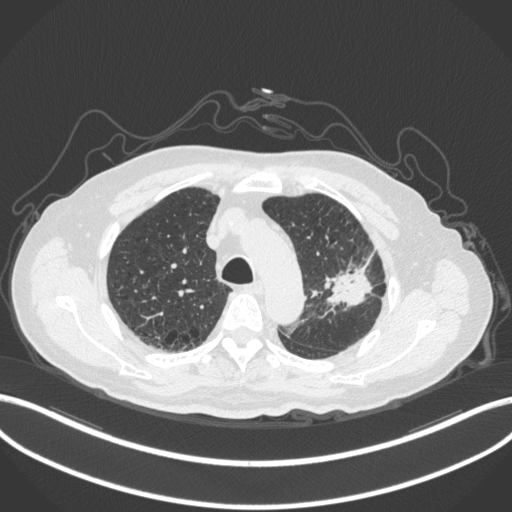
Chest CT, one axial slice. Slice 223 of 331 in the series (ordered by position). 120 kVp. Lung window (W 1500 / L -600 HU). 1 mm slice thickness. 512 × 512 image matrix, field of view 400 × 400 mm. Male patient, age 79 years. From the clinical record (not read from this slice): clinical TNM (as recorded): T2a N1 M1; histopathological grade: G3.
Structures marked on this image (bounding box drawn by a radiologist):
- lung tumour (recorded histology: adenocarcinoma): box from (x=327, y=257) to (x=373, y=309) px